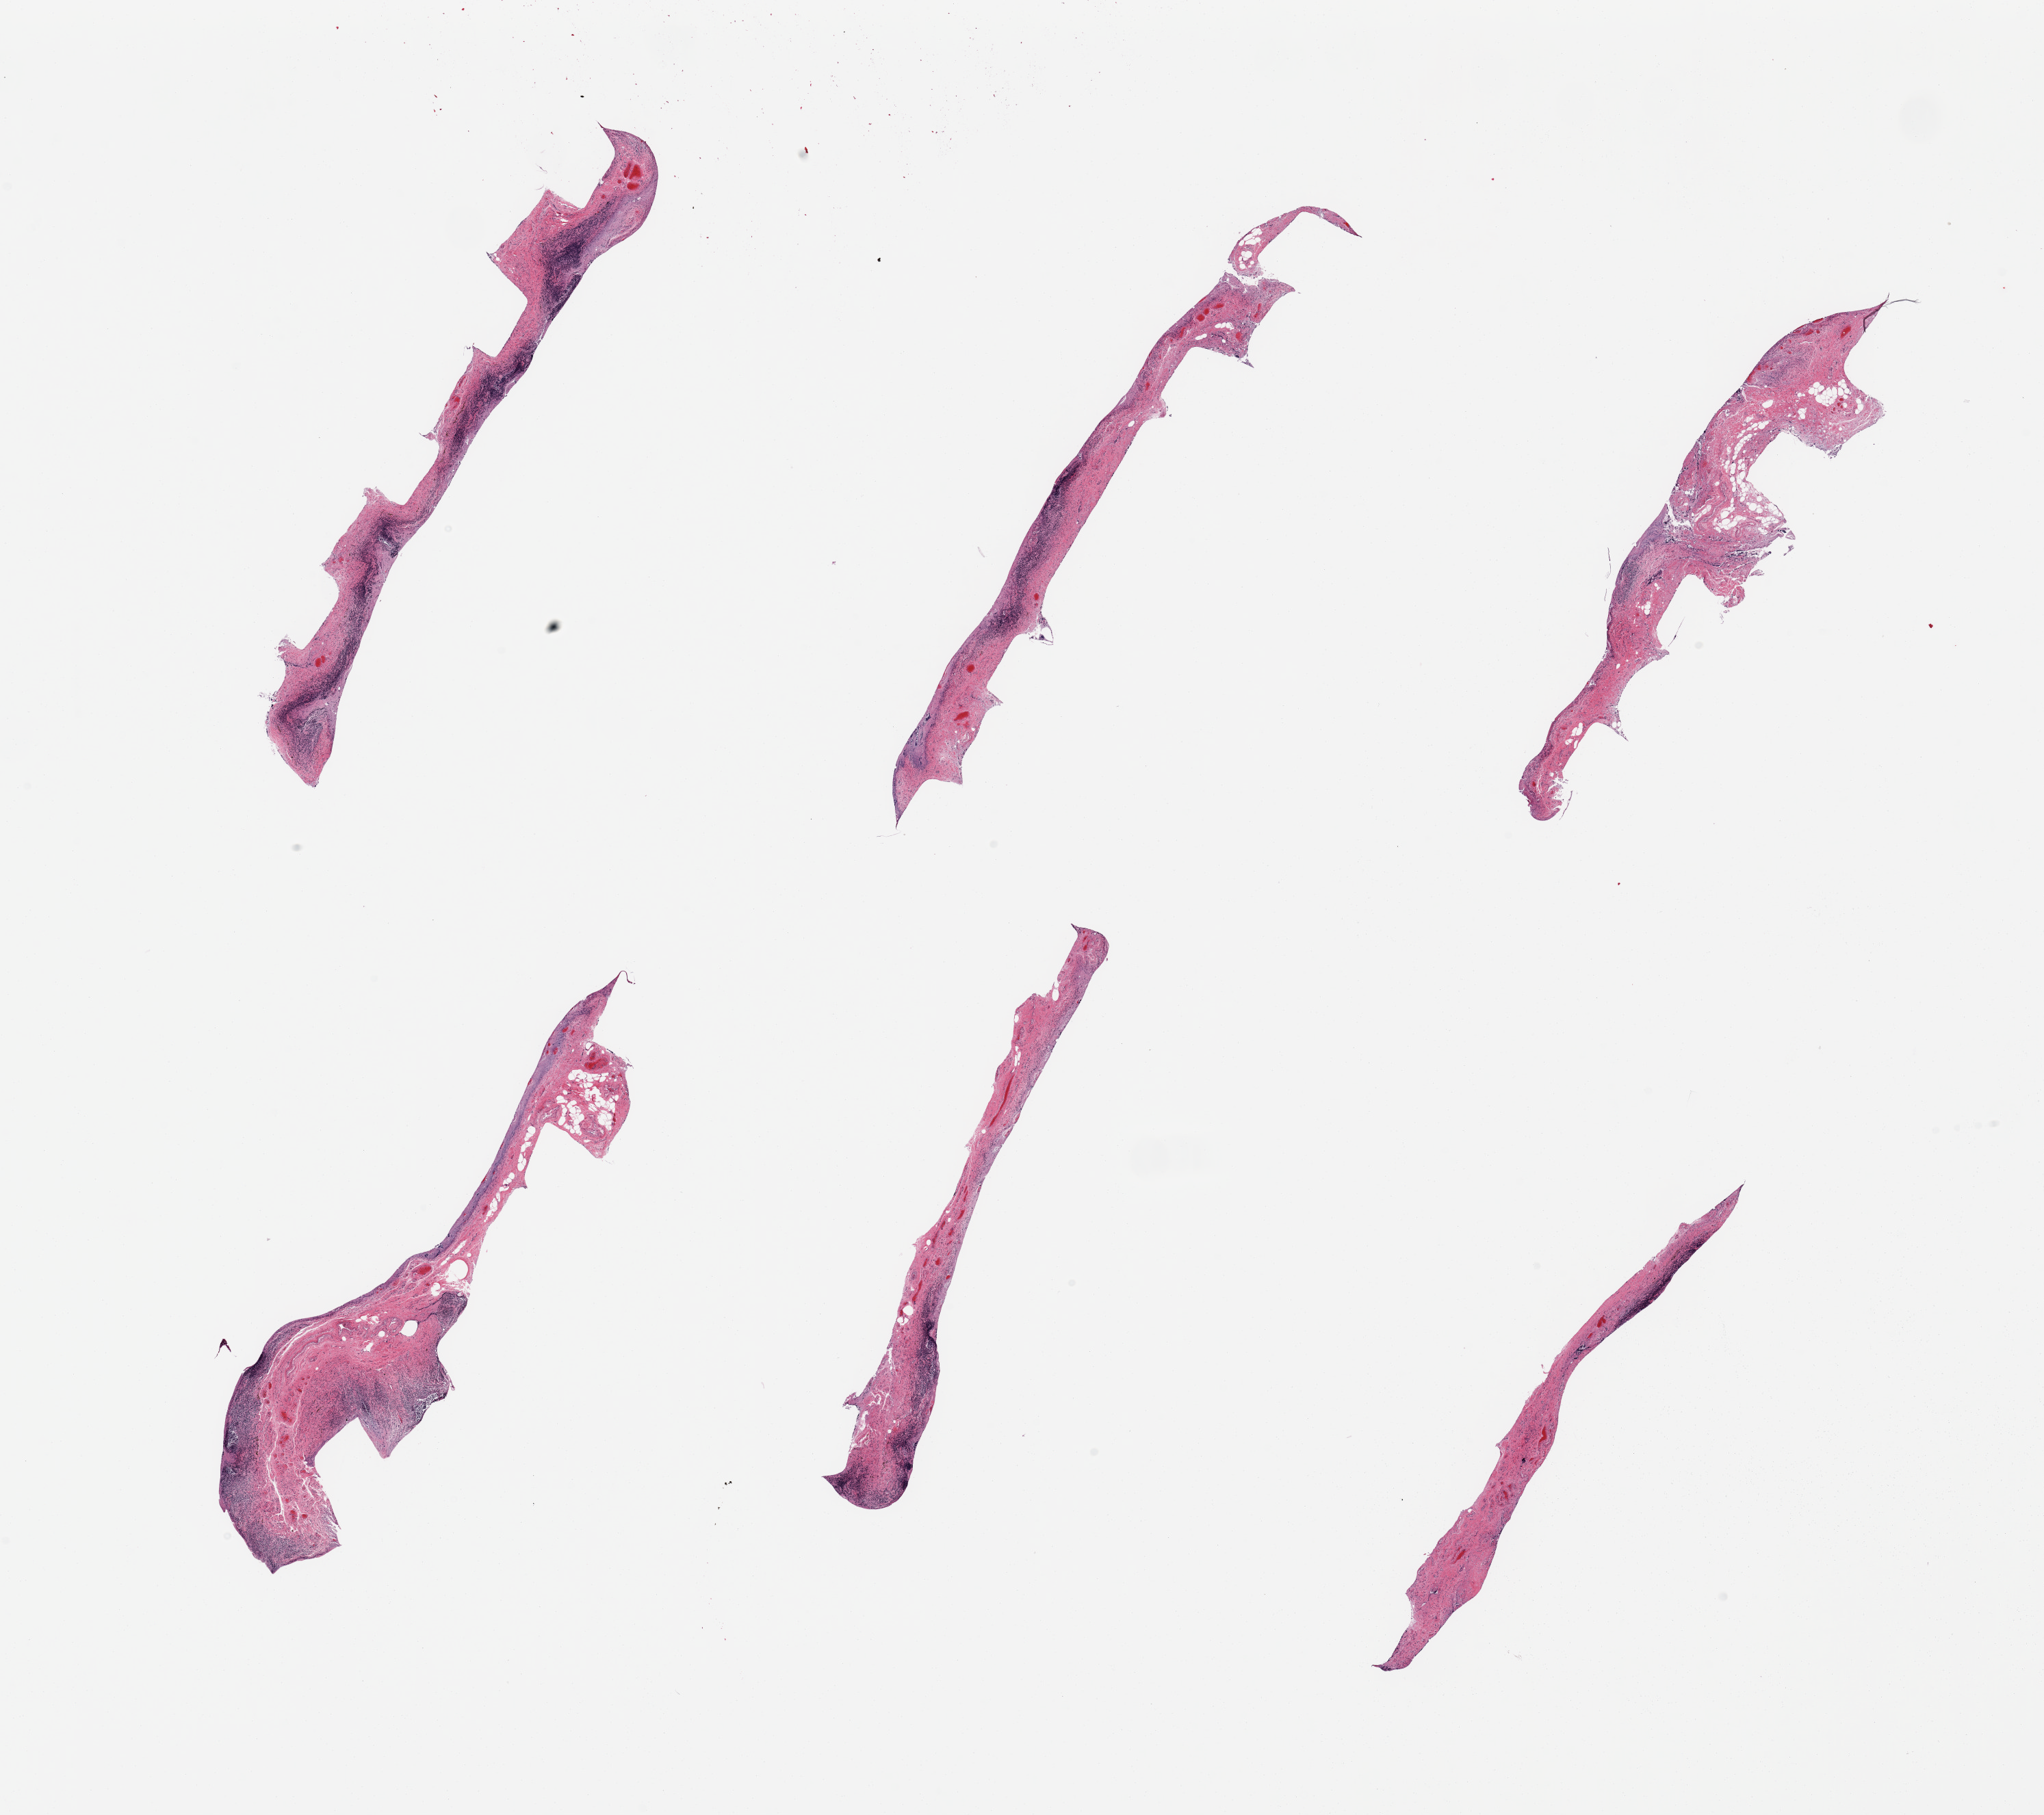
Whole-slide image, hematoxylin and eosin (H&E) stain — a low-resolution overview of the entire scanned area, about 23.6 x 21.0 mm (acquisition: 20x scan). PAXgene-fixed paraffin-embedded (PFPE) section. Target tissue: ileum. Tissue donor sample. Donor sex: male.
- pathologist's review note for this sample: 6 pieces; autolyzed mucosa with residual lymphoid tissue comprising 20-50%